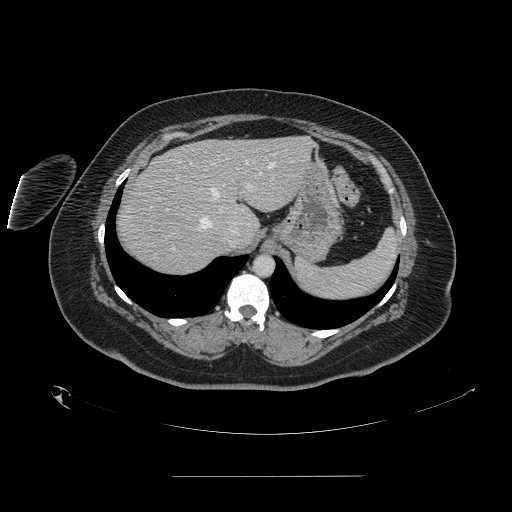
Contrast-enhanced abdominal CT, one axial slice; position 118 of 164 along the scan axis; 120 kVp; intravenous contrast given; soft-tissue window (W 400 / L 40 HU); 512 × 512 image matrix, field of view 495 × 495 mm. Female patient, age 52 years. From the clinical record (not read from this slice): diagnosis: colorectal cancer liver metastases, imaged before liver resection; multiple liver metastases: yes; largest metastasis: 3.5 cm; chemotherapy before resection: no.
Structures marked on this image (expert manual segmentation):
- hepatic veins: bounding box <196,161,274,230> (left, top, right, bottom; pixels)
- liver: <117,137,312,275>
- planned liver remnant (the part of the liver to remain after resection): <169,137,312,226>
- portal vein (with intrahepatic branches): <176,178,252,211>